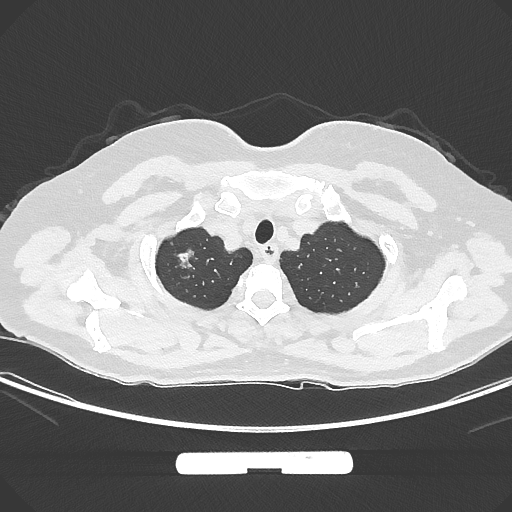
Chest CT, one axial slice. Slice 262 of 294 in the series (ordered by position). Lung window (W 1500 / L -600 HU). 512 × 512 image matrix, field of view 369 × 369 mm. Patient: female, 58 years. From the clinical record (not read from this slice): clinical TNM (as recorded): T1b N0 M0.
Structures marked on this image (rectangle marked by the reading radiologist):
- lung tumour (recorded histology: adenocarcinoma): bounding box <172,248,201,272> (left, top, right, bottom; pixels)